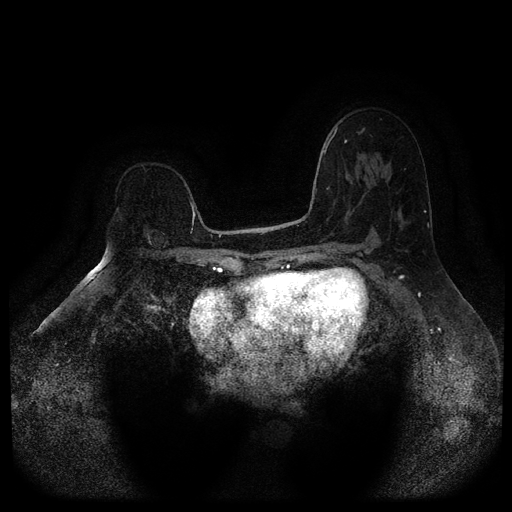
Breast MRI (dynamic contrast-enhanced, multi-phase), one axial slice. Slice 67 of 116 in the series (ordered by position). Dynamic contrast-enhanced series, time point 2 of 5 at this slice position (early post-contrast). 1.5 T. TE 2.6 ms, TR 5.4 ms. 512 × 512 image matrix, field of view 340 × 340 mm. Patient: female, 64 years.
Structures marked on this image (semi-automatically segmented with operator editing):
- breast lesion (labelled benign in the annotation): box from (x=143, y=228) to (x=169, y=253) px